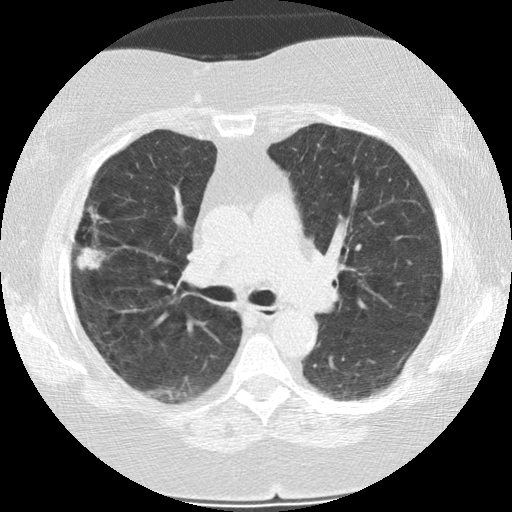
Chest CT (low-dose screening protocol), one axial image, baseline annual screen, lung window (W 1500 / L -600 HU), slice 75 of 187 in the series. Female, age 73 years at enrolment.
Expert reader's lesion annotation, box from (x=59, y=212) to (x=113, y=276) px. Reader record for this screening exam (exam-level; its link to the box is not recorded): non-calcified nodule or mass ≥4 mm, right upper lobe, 21 × 14 mm, poorly defined margins, soft tissue attenuation. Official screen result: positive, change unspecified: nodule(s) >= 4 mm or enlarging nodule(s), mass(es), or other non-specific abnormalities suspicious for lung cancer. Later outcome: lung cancer diagnosed 482 days after this screen — bronchiolo-alveolar adenocarcinoma, NOS, right upper lobe, moderately differentiated (G2), stage IIIB (AJCC 6th edition), 21 mm at pathology.